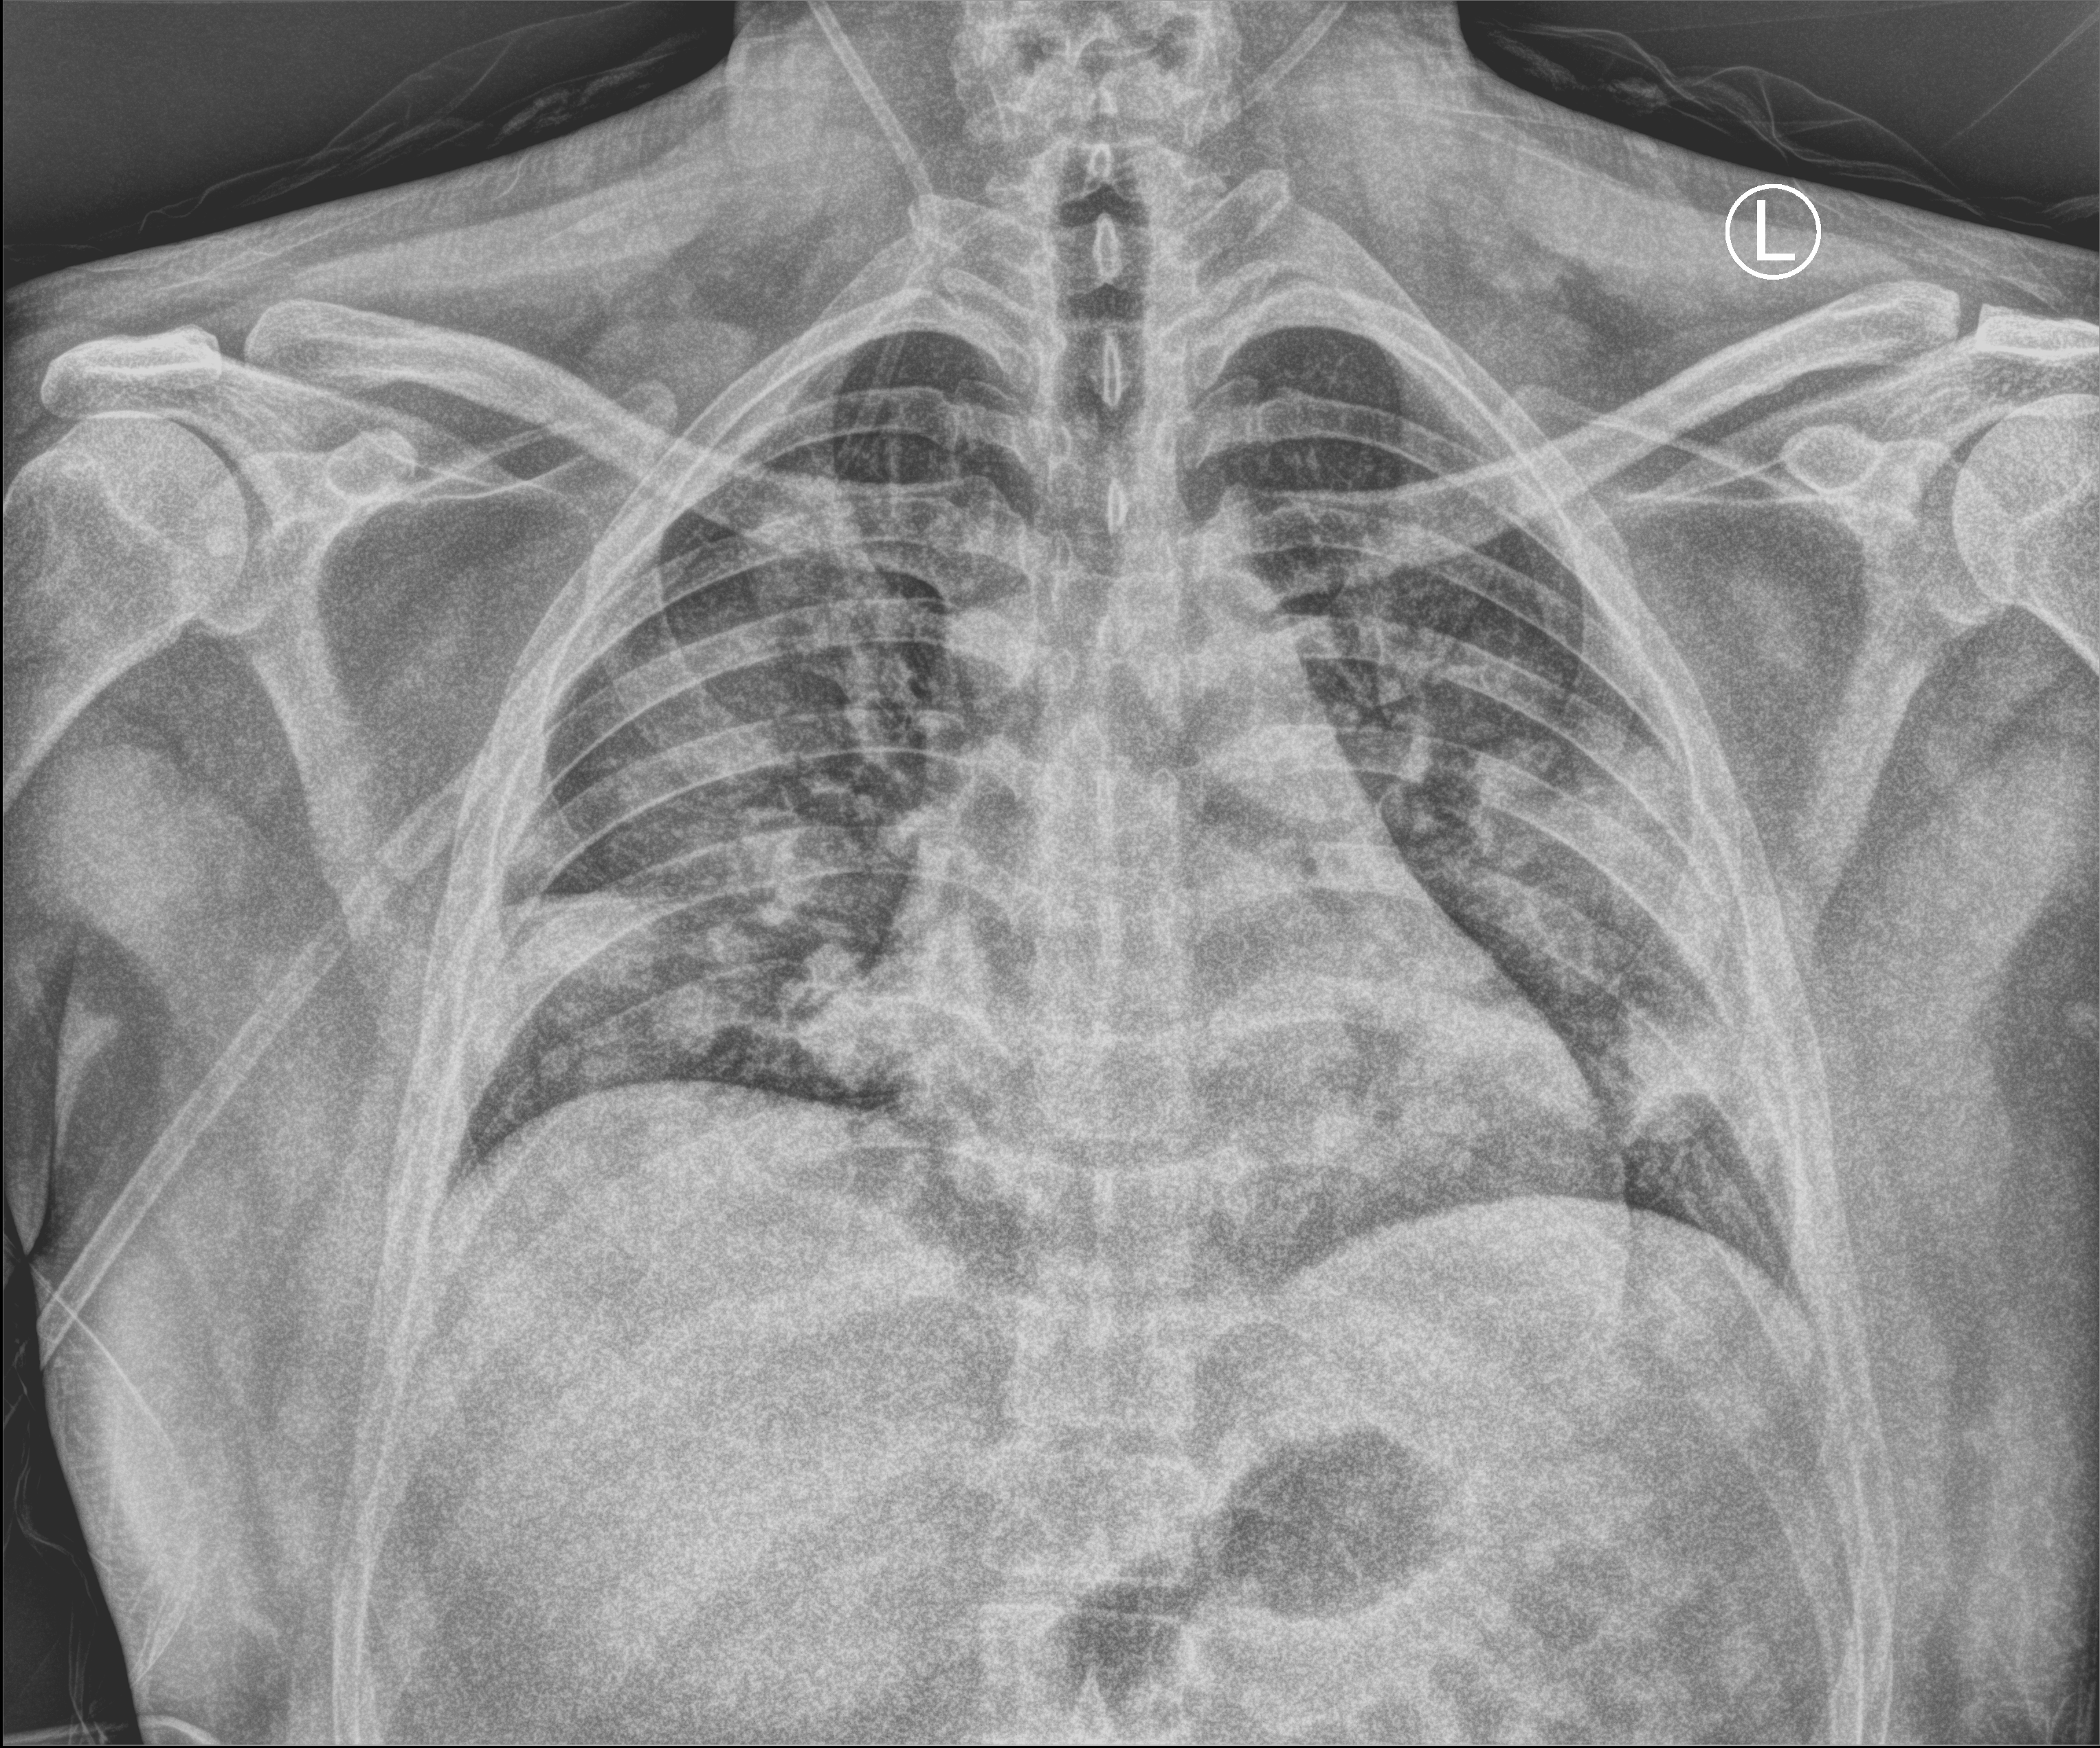
Portable chest radiograph. Male patient hospitalised with COVID-19, age 18–59 years.
Admission-level facts for this patient (not findings on this image; timing relative to this image not recorded): mechanically ventilated during this hospital stay: no; other chronic lung disease (admission record): no.